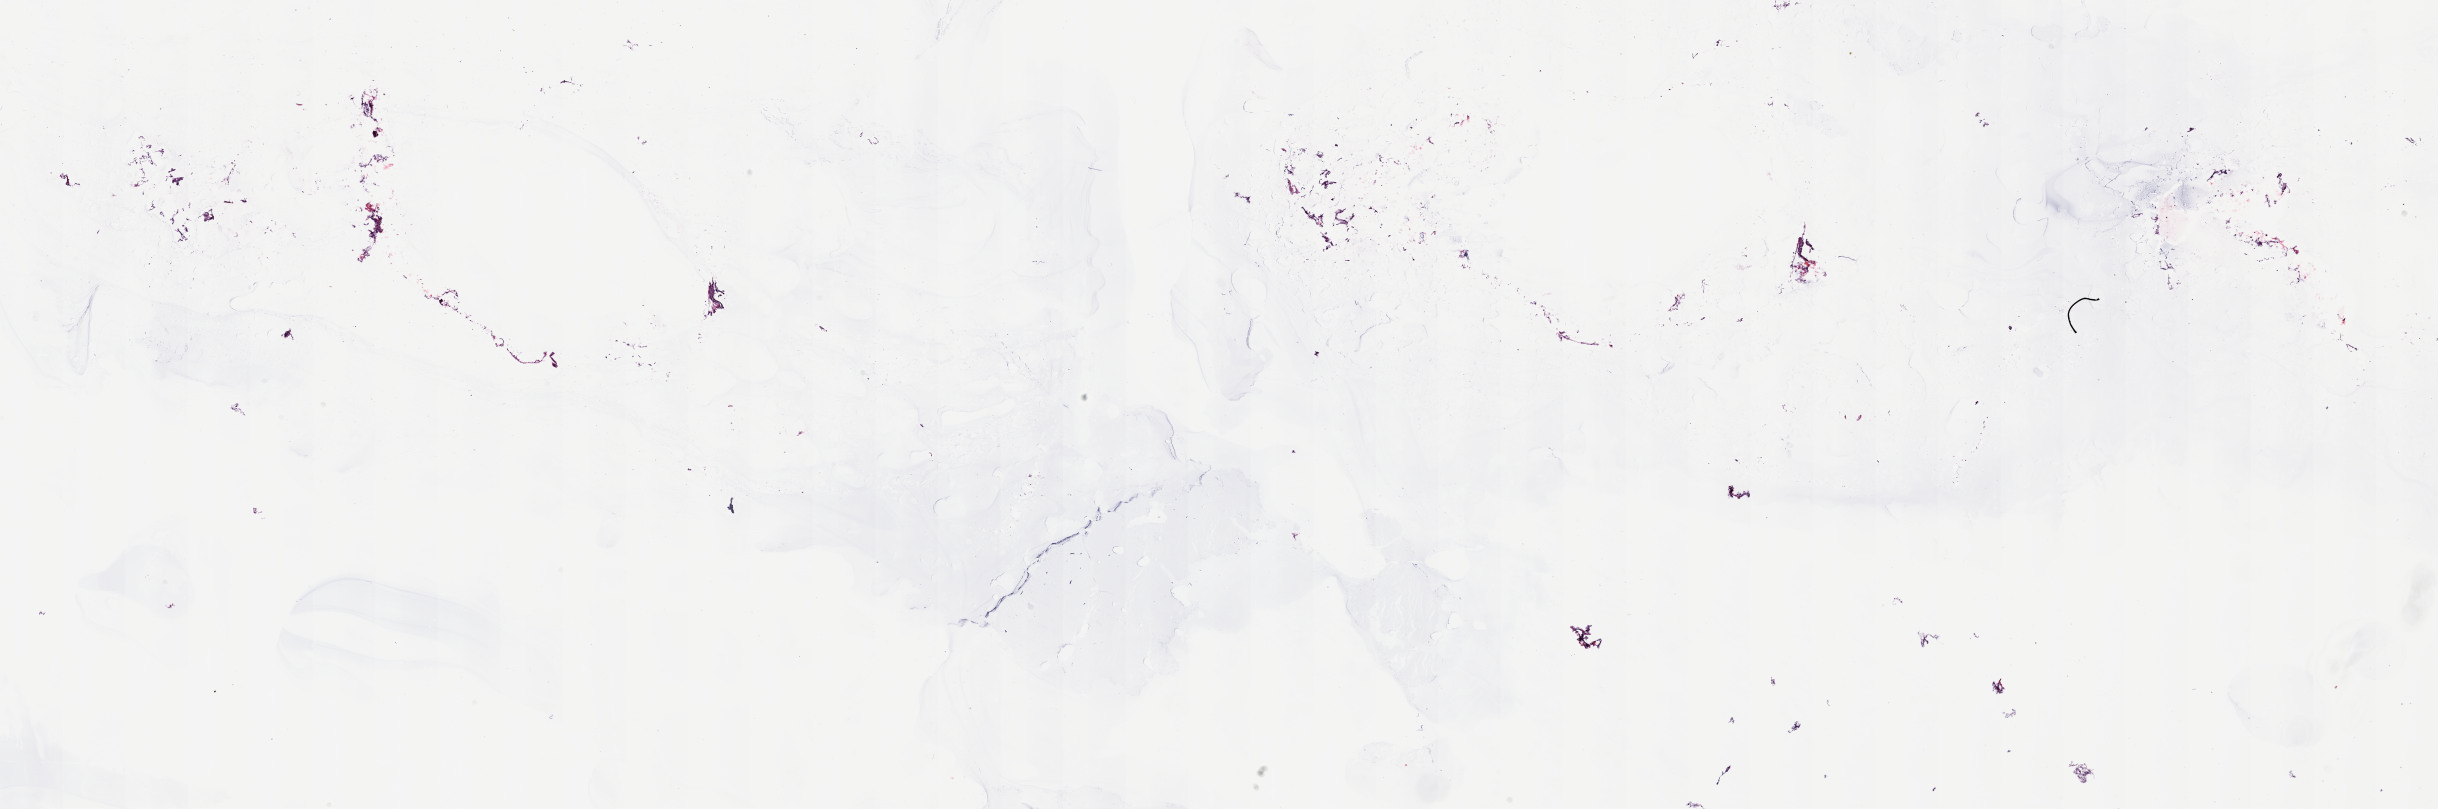
H&E-stained whole-slide image, a low-resolution overview of the entire scanned area, about 38.7 x 12.8 mm (slide scanned at 20x), frozen section from the top of the tissue portion, solid tissue normal (non-tumour tissue) sample from the thymus. Male patient; age at initial diagnosis 66 years. Pathologist review of this section (percent, as recorded): tumour cells 0%, tumour nuclei 0%.
This section: solid tissue normal sample (biorepository sample class). Patient diagnosis: Thymoma, type A, malignant.